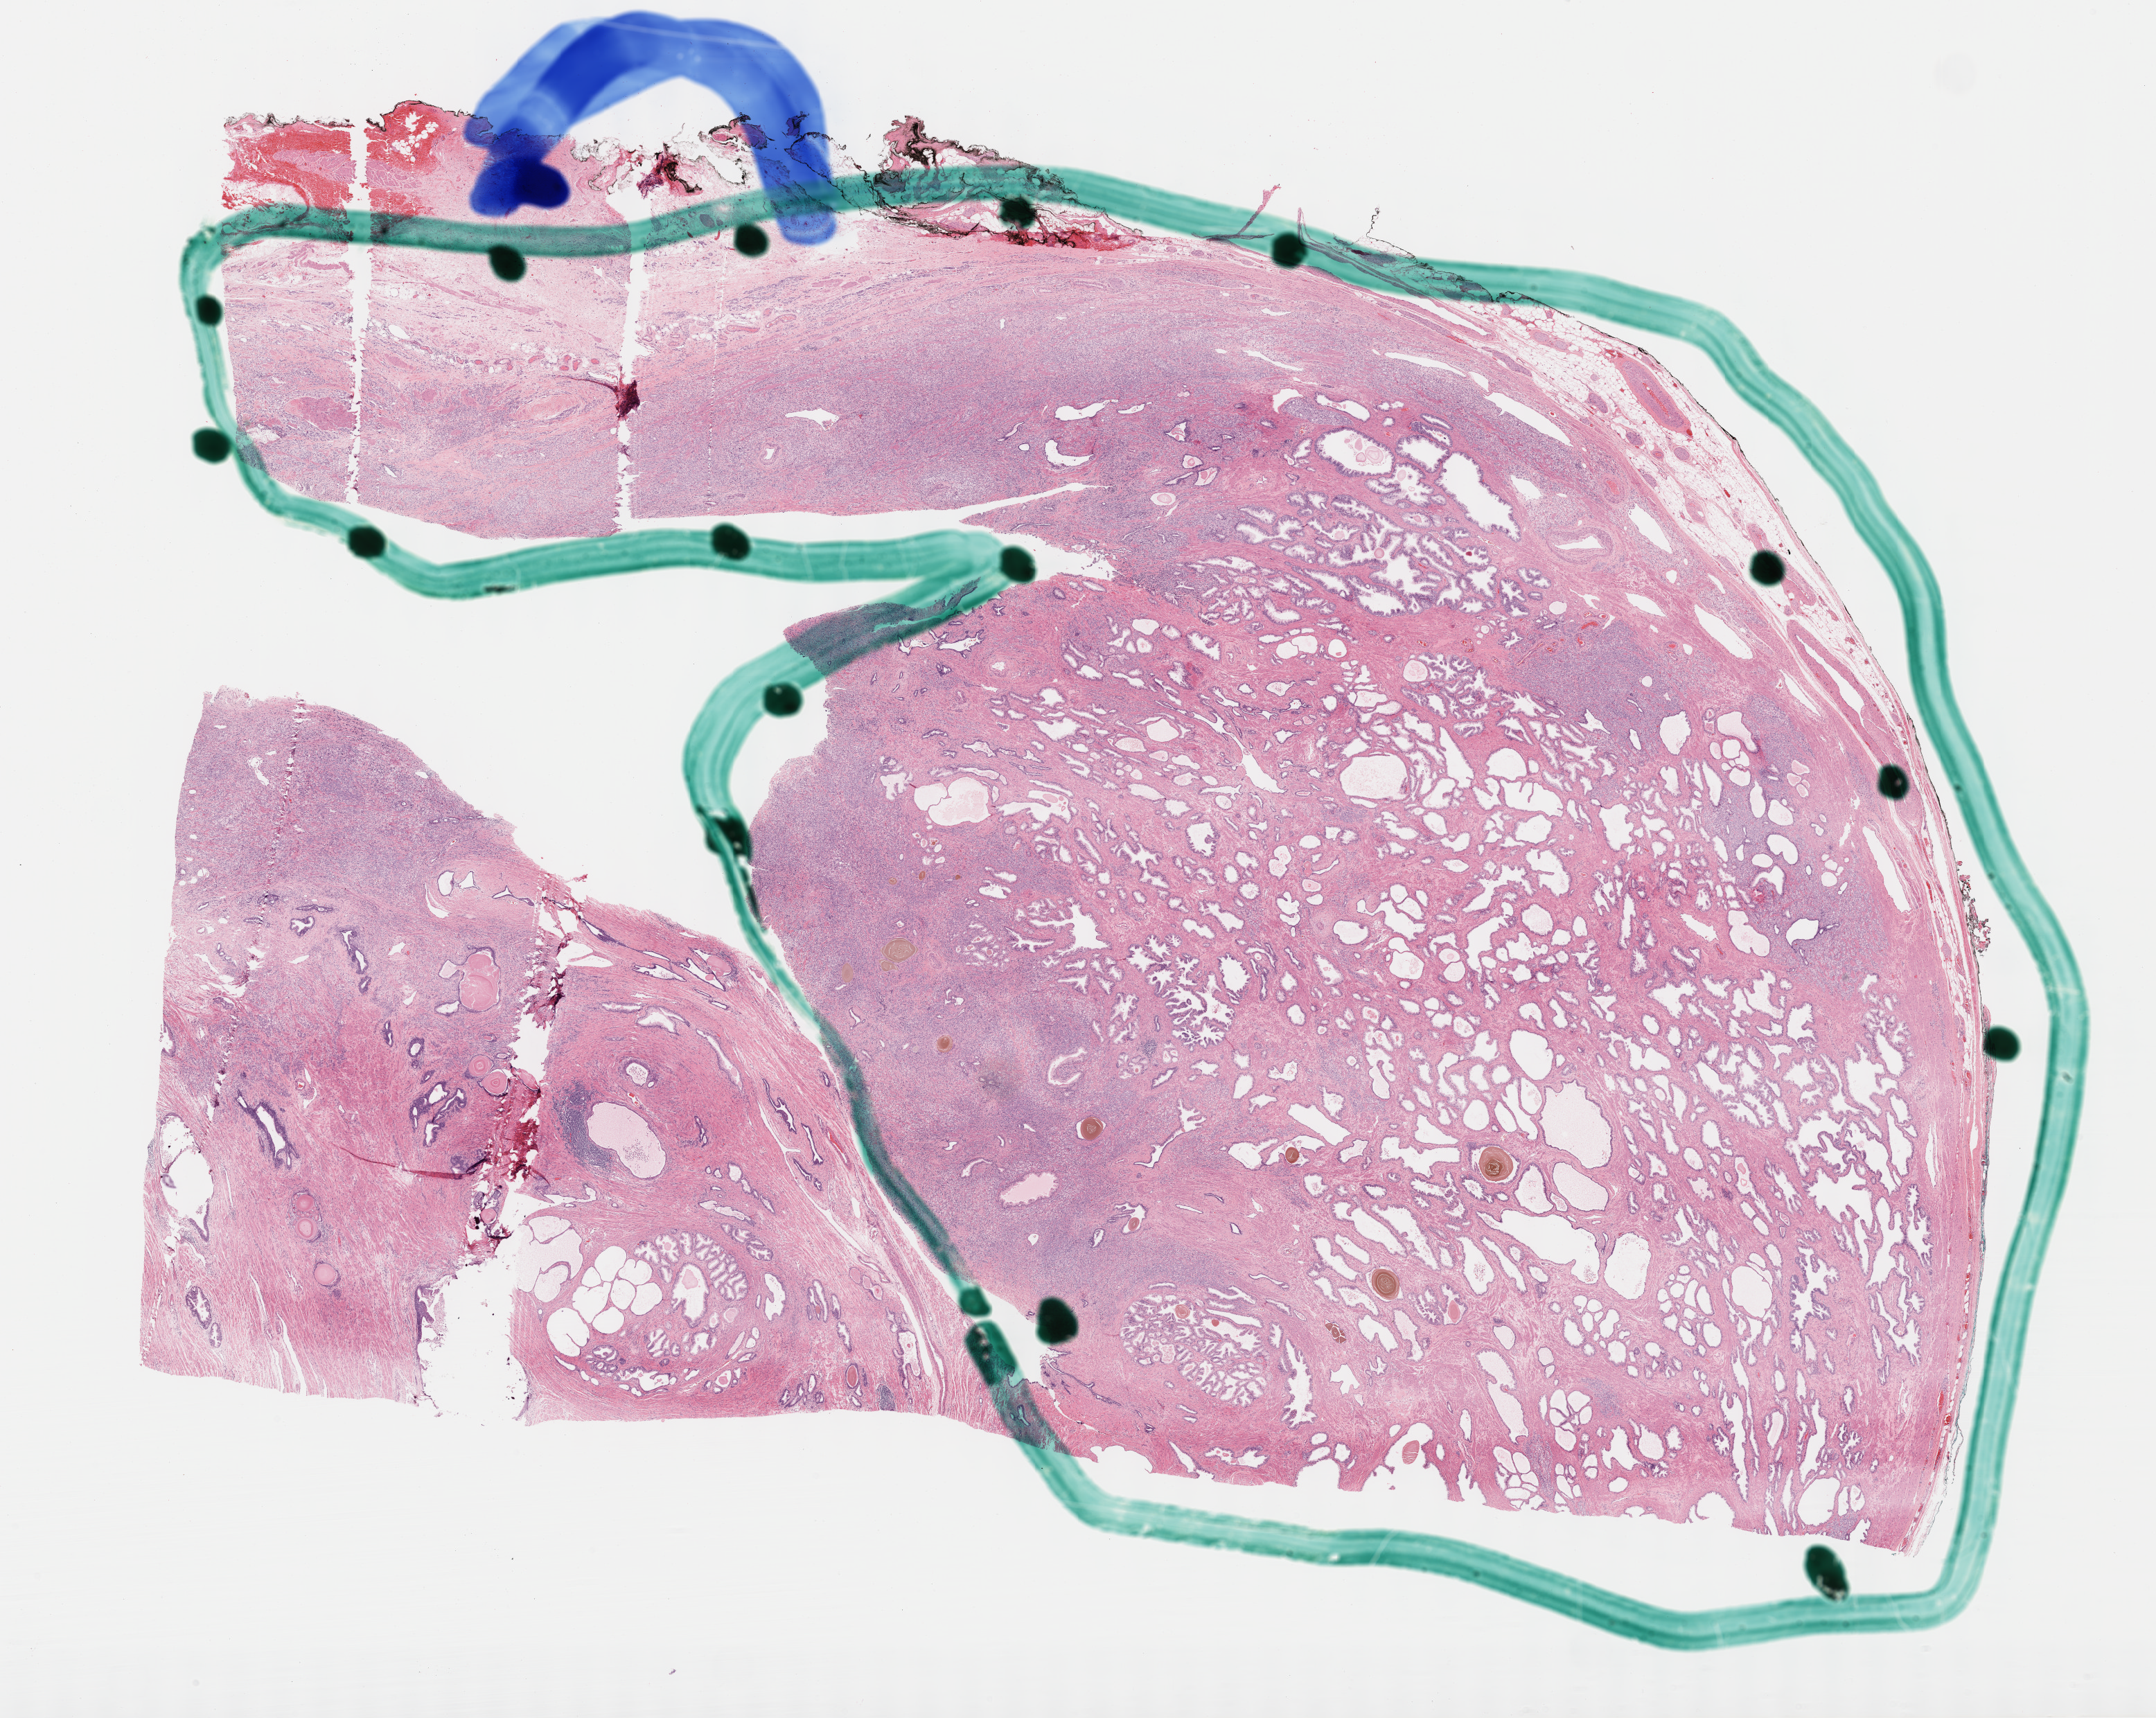
Whole-slide histology image, H&E — shown as a low-resolution overview of the whole scanned area (about 25.2 x 20.1 mm), formalin-fixed paraffin-embedded (FFPE) diagnostic section, sample: primary tumour, prostate. Male, age 61 years at initial diagnosis. Gleason score: 9 (4+5).
Pathologic diagnosis: Adenocarcinoma, NOS (prostate gland). Lymph nodes positive (case pathology): 1 of 8 examined.